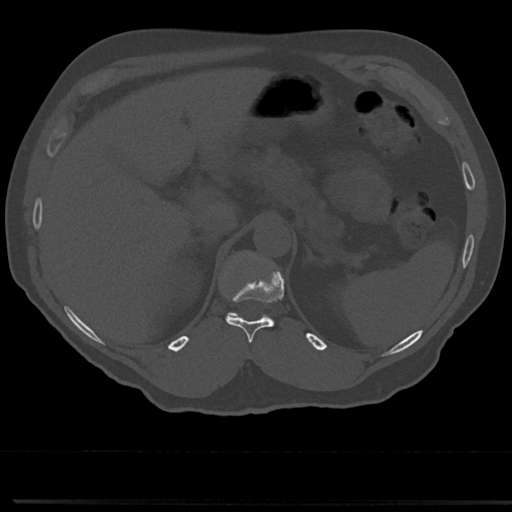
CT including the spine, one axial slice. Slice 187 of 817 in the series (ordered by position). 120 kVp. Bone window (W 1800 / L 400 HU). 512 × 512 image matrix. Patient: male, 61 years. From the clinical record (not read from this slice): primary cancer: prostate.
Annotated regions visible in this slice (semi-automatically segmented with operator editing):
- T11 vertebra: bounding box (x1, y1, x2, y2) in pixels: (226, 274, 283, 344)
- T12 vertebra: (226, 255, 283, 320)